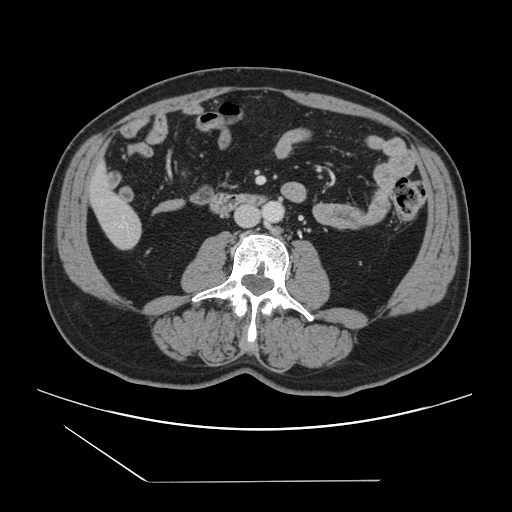
Contrast-enhanced abdominal CT, one axial slice. Position 21 of 157 along the scan axis. 120 kVp. Intravenous contrast given. Soft-tissue window (W 400 / L 40 HU). 512 × 512 image matrix, field of view 407 × 407 mm. Male patient, age 61 years. From the clinical record (not read from this slice): diagnosis: colorectal cancer liver metastases, imaged before liver resection; multiple liver metastases: yes; largest metastasis: 5.5 cm; chemotherapy before resection: no.
Annotated regions visible in this slice (manually delineated by an expert):
- liver: bounding box [x1, y1, x2, y2] px = [91, 168, 142, 249]
- planned liver remnant (the part of the liver to remain after resection): [91, 168, 130, 218]